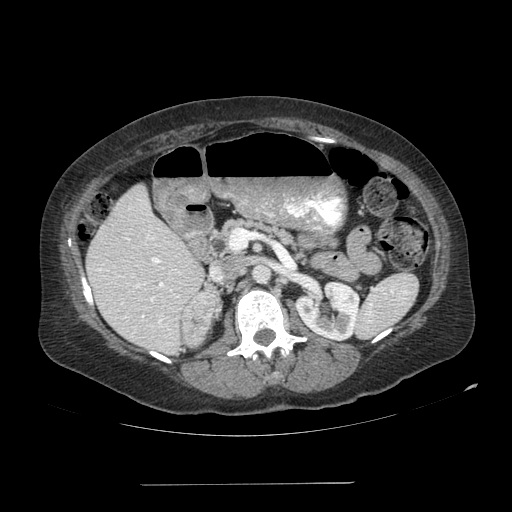
Contrast-enhanced abdominal CT, one axial slice. Slice 54 of 113 in the series (ordered by position). Reconstruction kernel SOFT. 120 kVp. Soft-tissue window (W 400 / L 40 HU). 512 × 512 image matrix, field of view 440 × 440 mm. Patient: female, 67 years. Case-level facts recorded for this patient, not image findings: diagnosis: adrenocortical carcinoma; tumour side: right adrenal; tumour size at pathology: 9.8 cm; Ki-67 index: 59 %; stage (as recorded): 4.
Annotated regions visible in this slice (semi-automatically segmented with operator editing):
- mass: bounding box [x1, y1, x2, y2] px = [183, 295, 216, 346]